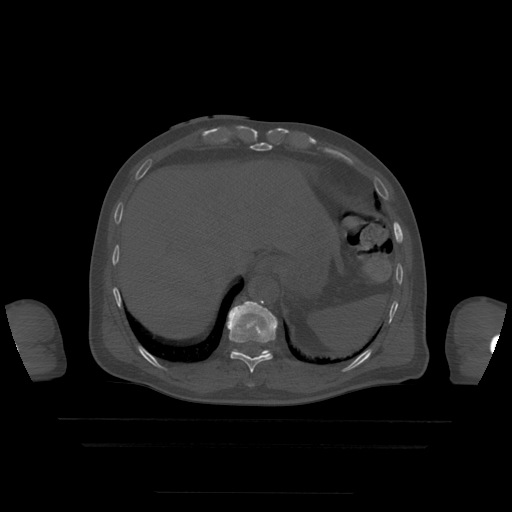
CT including the spine, one axial slice; slice 236 of 522 in the series (ordered by position); bone window (W 1800 / L 400 HU); 512 × 512 image matrix, field of view 436 × 436 mm. Patient age 68 years. From the clinical record (not read from this slice): primary cancer: urothelial.
Structures marked on this image (semi-automatically segmented with operator editing):
- T10 vertebra: bounding box <227,301,278,373> (left, top, right, bottom; pixels)
- T11 vertebra: <234,302,269,356>
- T9 vertebra: <249,385,253,387>